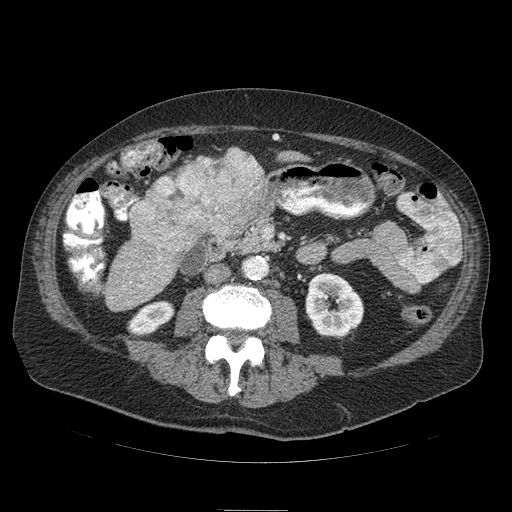
Contrast-enhanced abdominal CT (liver protocol), one axial slice; position 20 of 103 along the scan axis; reconstruction kernel STANDARD; soft-tissue window (W 400 / L 40 HU); 2.5 mm slice thickness; 512 × 512 image matrix, field of view 440 × 440 mm. From the clinical record (not read from this slice): diagnosis: hepatocellular carcinoma (patient treated with transarterial chemoembolisation; whether this scan precedes or follows treatment is not stated here); TNM stage (as recorded): Stage-IIIA.
Annotated regions visible in this slice (semi-automatic segmentation, software-assisted and operator-edited):
- liver parenchyma outside the tumour (the mass and vessels are separate outlines, so this box may not span the whole liver): box from (x=219, y=148) to (x=302, y=176) px
- mass: (x=128, y=149)–(x=272, y=267)